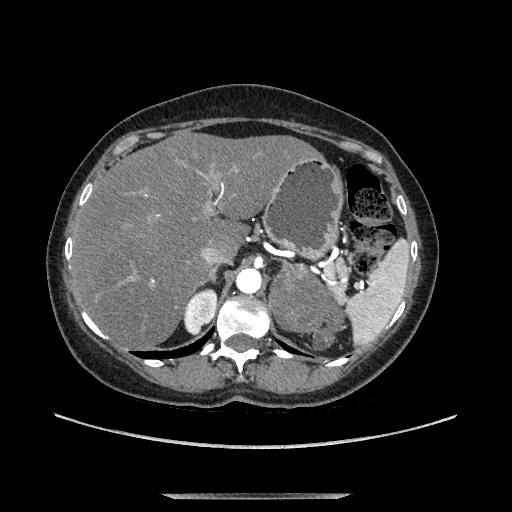
Contrast-enhanced abdominal CT, one axial slice. Soft-tissue window (W 400 / L 40 HU). 512 × 512 image matrix. Female patient. From the clinical record (not read from this slice): diagnosis: adrenocortical carcinoma; tumour side: left adrenal; tumour size at pathology: 9 cm; Ki-67 index: 2 %; stage (as recorded): 3.
Structures marked on this image (semi-automatic segmentation, software-assisted and operator-edited):
- mass: bounding box (x1, y1, x2, y2) in pixels: (271, 265, 342, 348)